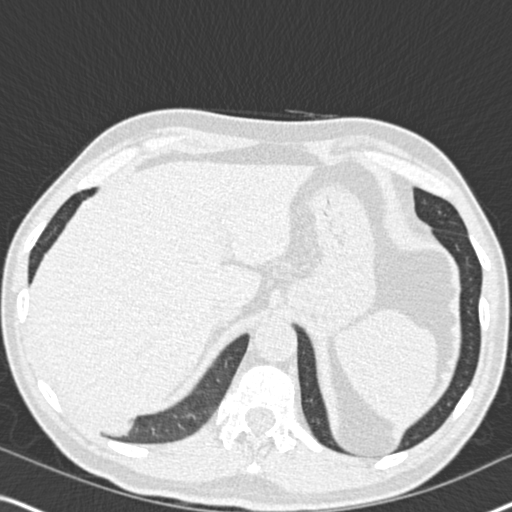
Low-dose screening chest CT, one axial slice; slice 43 of 182 in the series (ordered by position); 120 kVp; lung window (W 1500 / L -600 HU); 2 mm slice thickness; 512 × 512 image matrix, field of view 330 × 330 mm.
Outlined on this slice (manually delineated by an expert):
- lesion 1 (tumor, lower lobe of right lung): box from (x=80, y=416) to (x=130, y=435) px